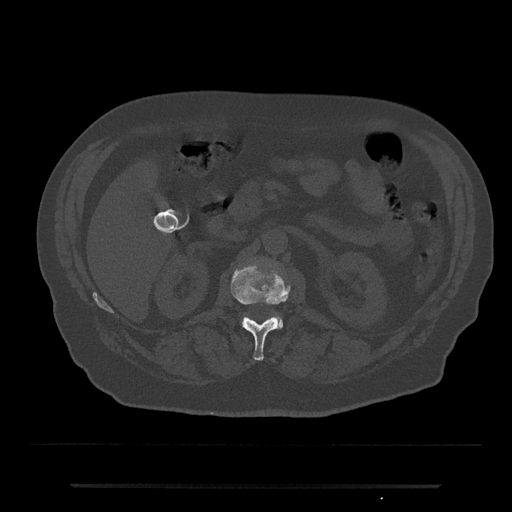
CT including the spine, one axial slice. Position 519 of 797 along the scan axis. Reconstruction kernel Br40s/3. 120 kVp. Bone window (W 1800 / L 400 HU). 0.5 mm slice thickness. 512 × 512 image matrix, field of view 434 × 434 mm. Male patient, age 80 years. From the clinical record (not read from this slice): primary cancer: prostate.
Outlined on this slice (semi-automatic segmentation, software-assisted and operator-edited):
- L1 vertebra: bounding box (x1, y1, x2, y2) in pixels: (231, 265, 289, 361)
- L2 vertebra: (273, 314, 284, 329)